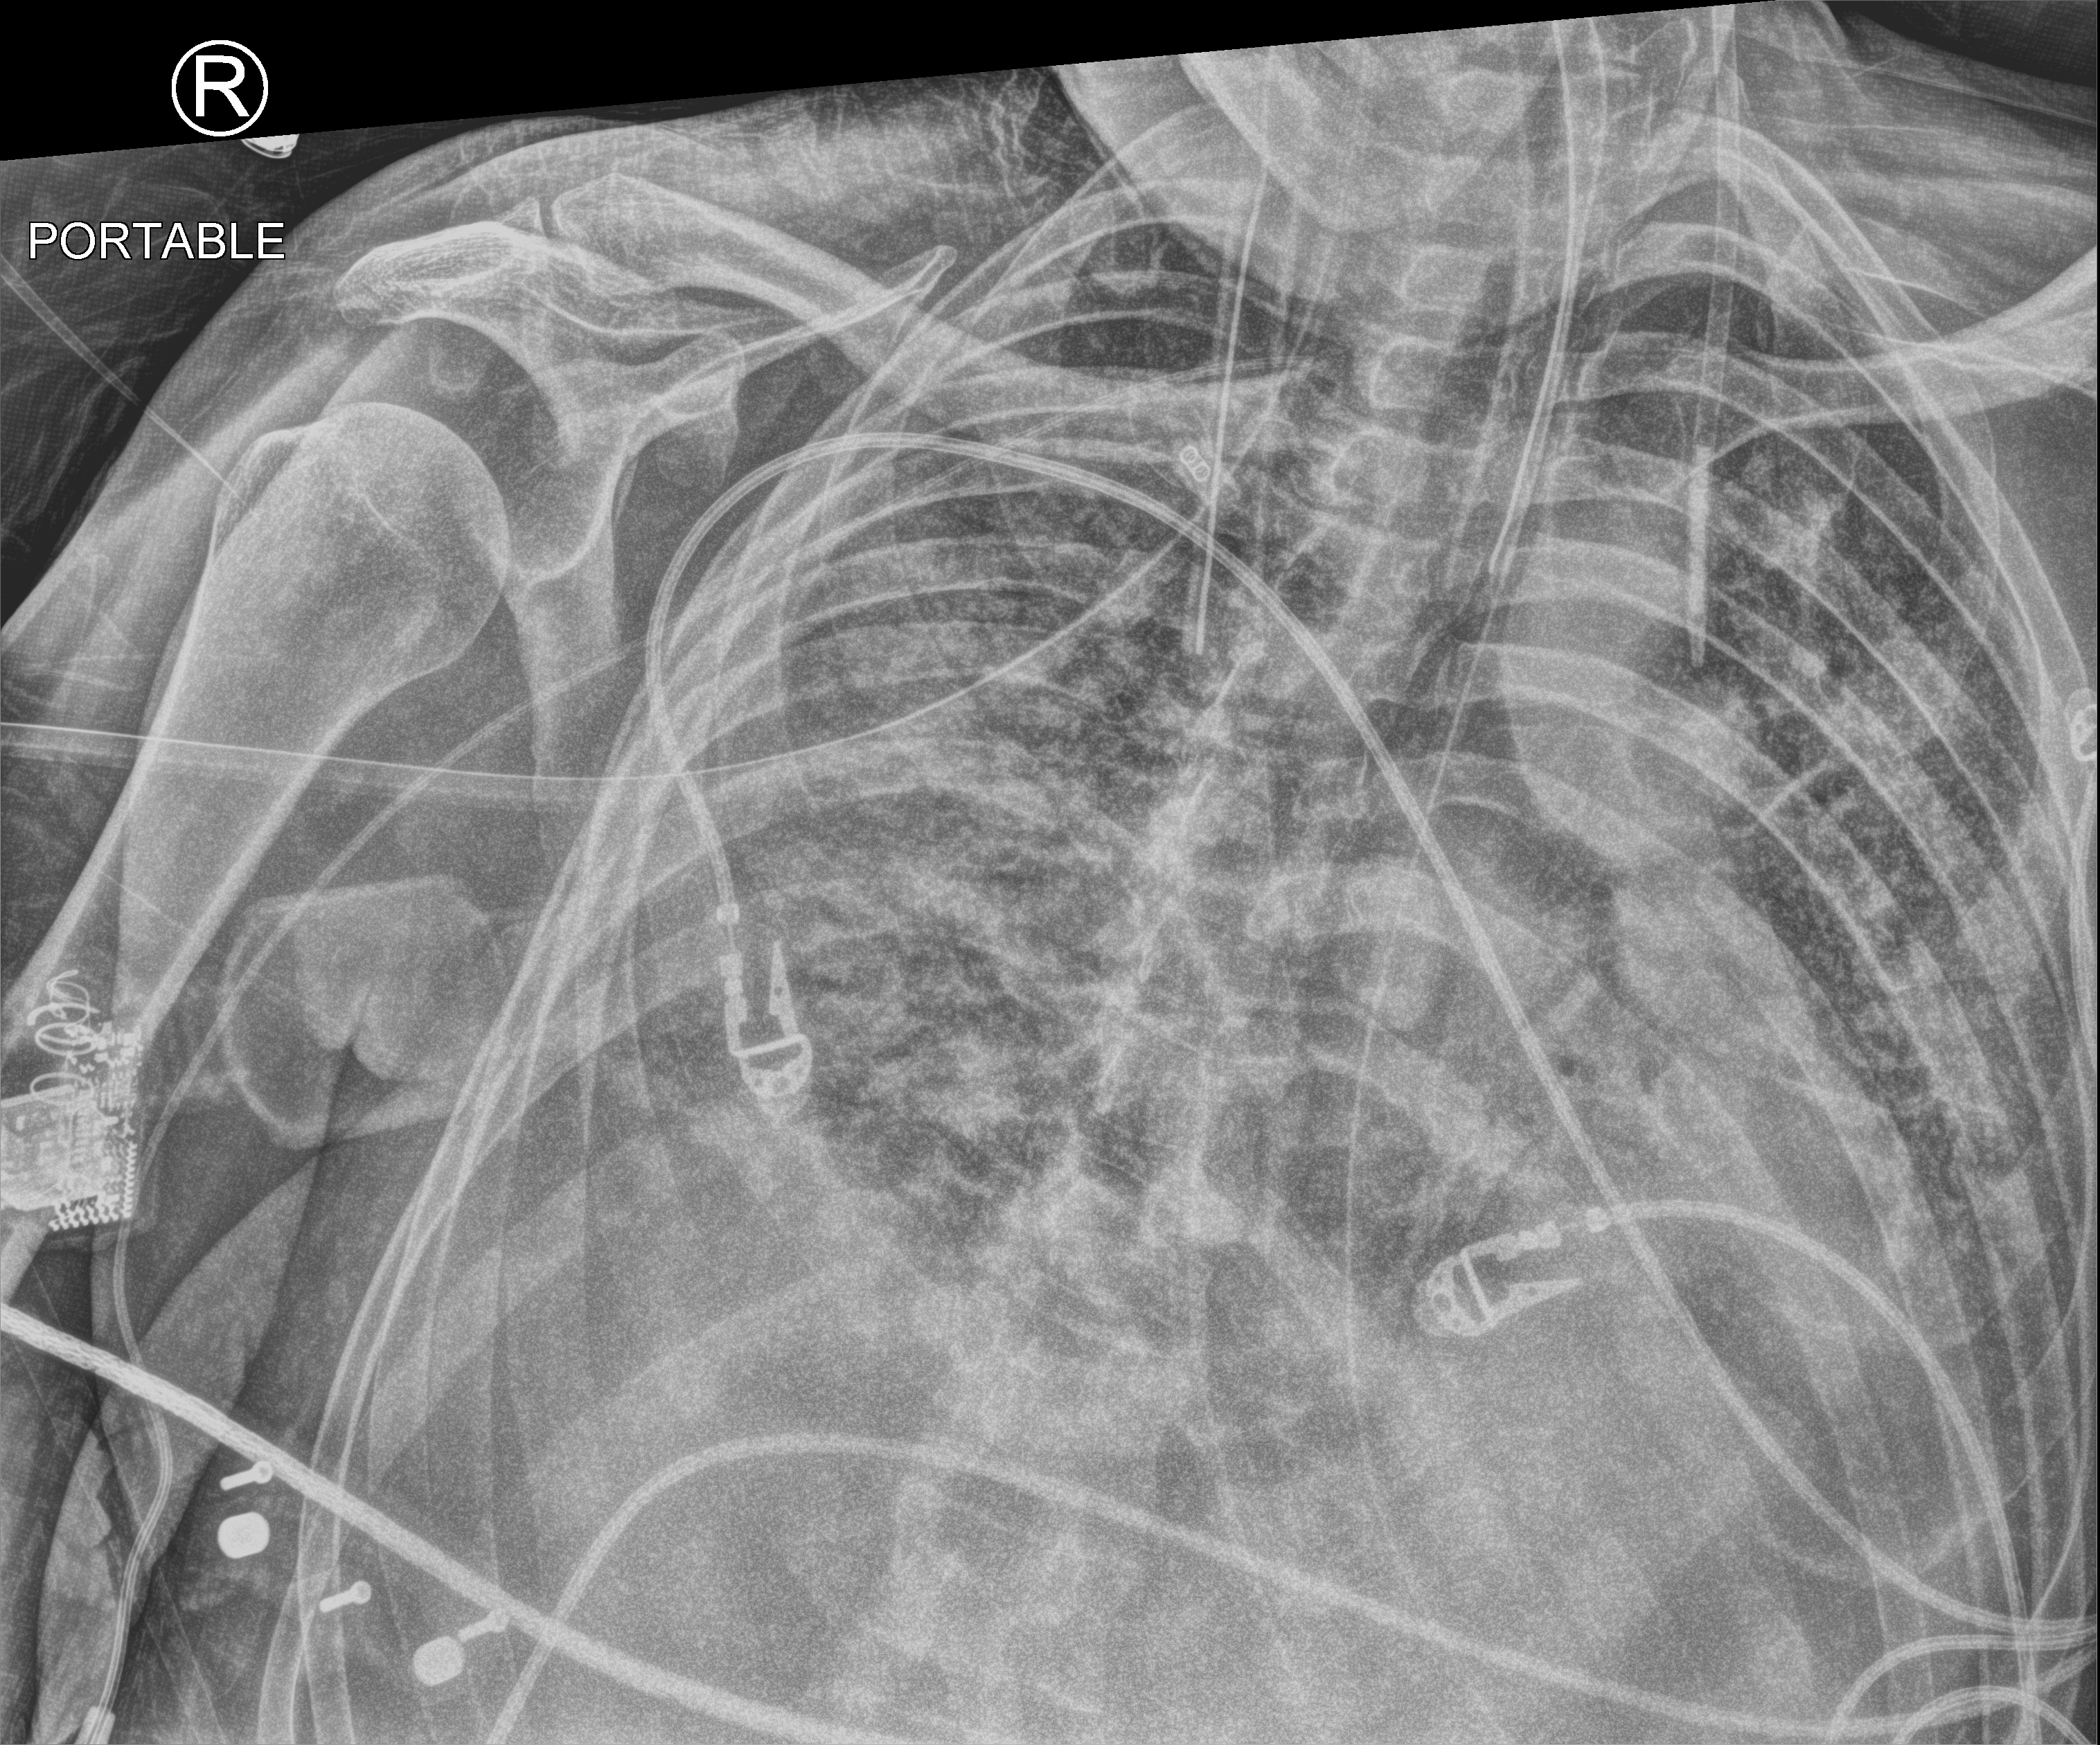
Bedside chest radiograph (computed radiography). Male patient hospitalised with COVID-19, age 18–59 years.
From the hospital-stay record, not from the radiograph (when in the stay this image was taken is not recorded): admitted to intensive care during this hospital stay: yes; mechanically ventilated during this hospital stay: yes.